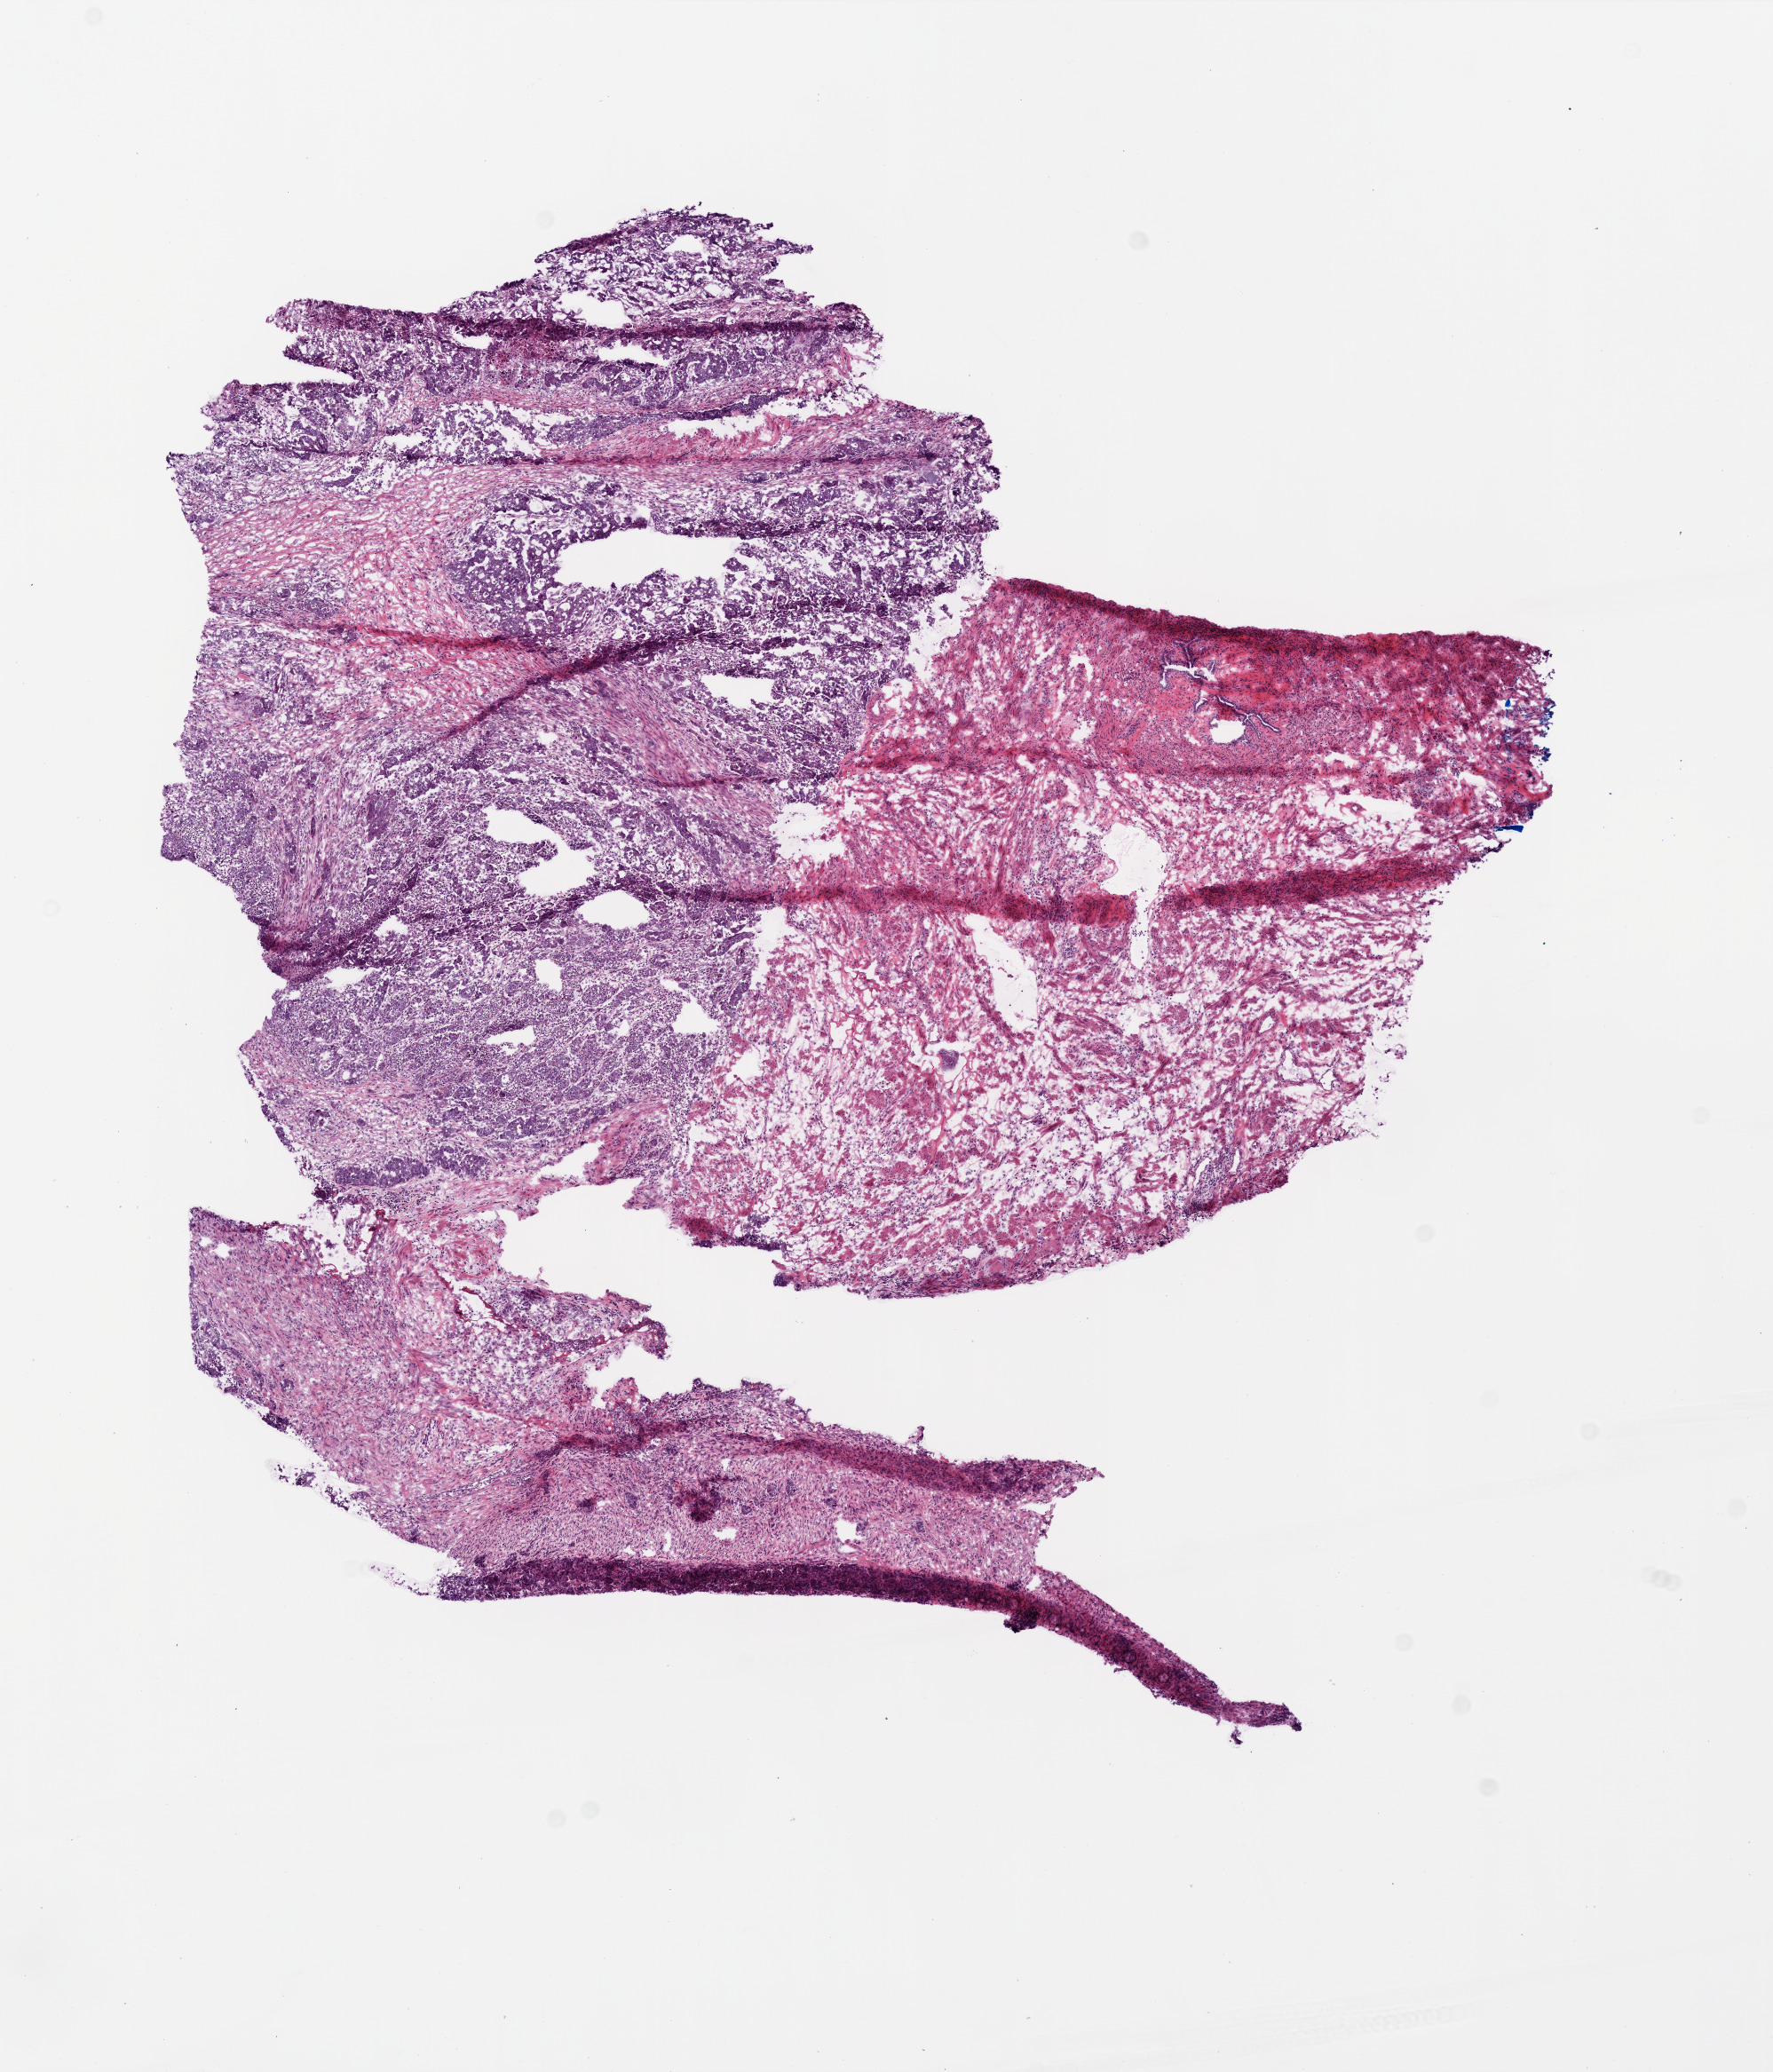
H&E-stained whole-slide image — low-resolution overview of the scanned area, about 8.0 x 9.3 mm (slide scanned at 20x), frozen section from the top of the tissue portion, ovary, primary tumour sample. Patient: female, age at initial diagnosis 83 years. Histologic grade: G3 (poorly differentiated). Slide review estimates, as recorded: tumour nuclei 80%, normal cells 0%, necrosis 0%.
Histologic diagnosis: Serous cystadenocarcinoma, NOS. FIGO stage: IIIC.